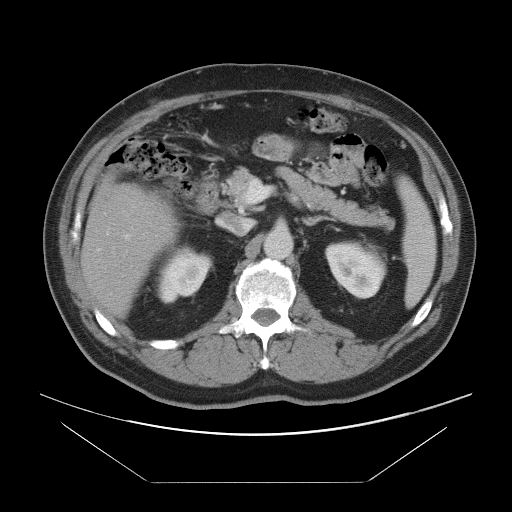
Contrast-enhanced abdominal CT, one axial slice. Position 46 of 97 along the scan axis. Intravenous contrast given. Soft-tissue window (W 400 / L 40 HU). 5 mm slice thickness. 512 × 512 image matrix, field of view 442 × 442 mm. Male patient, age 62 years. Case-level facts recorded for this patient, not image findings: diagnosis: colorectal cancer liver metastases, imaged before liver resection; multiple liver metastases: no; largest metastasis: 7 cm; disease in both lobes: yes.
Annotated regions visible in this slice (outlined manually by an expert reader):
- hepatic veins: bounding box [x1, y1, x2, y2] px = [106, 231, 114, 248]
- liver: [83, 182, 172, 315]
- planned liver remnant (the part of the liver to remain after resection): [83, 181, 173, 315]
- portal vein (with intrahepatic branches): [124, 235, 129, 238]